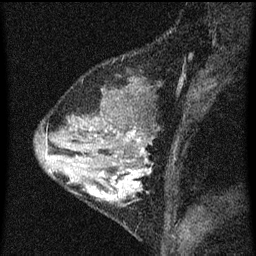
Breast MRI (dynamic contrast-enhanced), one sagittal slice. Position 24 of 60 along the scan axis. Dynamic contrast-enhanced series, image 2 of 3 at this slice position (ordered by acquisition). 1.5 T. TE 4.2 ms, TR 8 ms. 2 mm slice thickness. 256 × 256 image matrix, field of view 180 × 180 mm. Patient: female, 33 years.
Annotated regions visible in this slice (semi-automatically segmented with operator editing):
- analysis volume of interest (the breast-tissue region the enhancement analysis was run in; not a lesion): bounding box (x1, y1, x2, y2) in pixels: (67, 118, 154, 215)
- tumour enhancement mask (voxels above the 70 % enhancement threshold inside the analysis volume of interest): (90, 130, 151, 199)